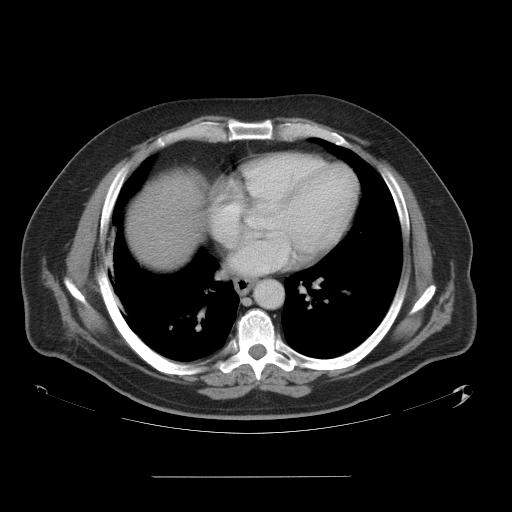
Contrast-enhanced abdominal CT, one axial slice. Position 55 of 58 along the scan axis. Intravenous contrast given. Soft-tissue window (W 400 / L 40 HU). 512 × 512 image matrix, field of view 480 × 480 mm. Male patient, age 63 years. Case-level facts recorded for this patient, not image findings: diagnosis: colorectal cancer liver metastases, imaged before liver resection; multiple liver metastases: no.
Annotated regions visible in this slice (manually delineated by an expert):
- liver: bounding box [x1, y1, x2, y2] px = [128, 172, 202, 269]
- planned liver remnant (the part of the liver to remain after resection): [128, 225, 192, 269]